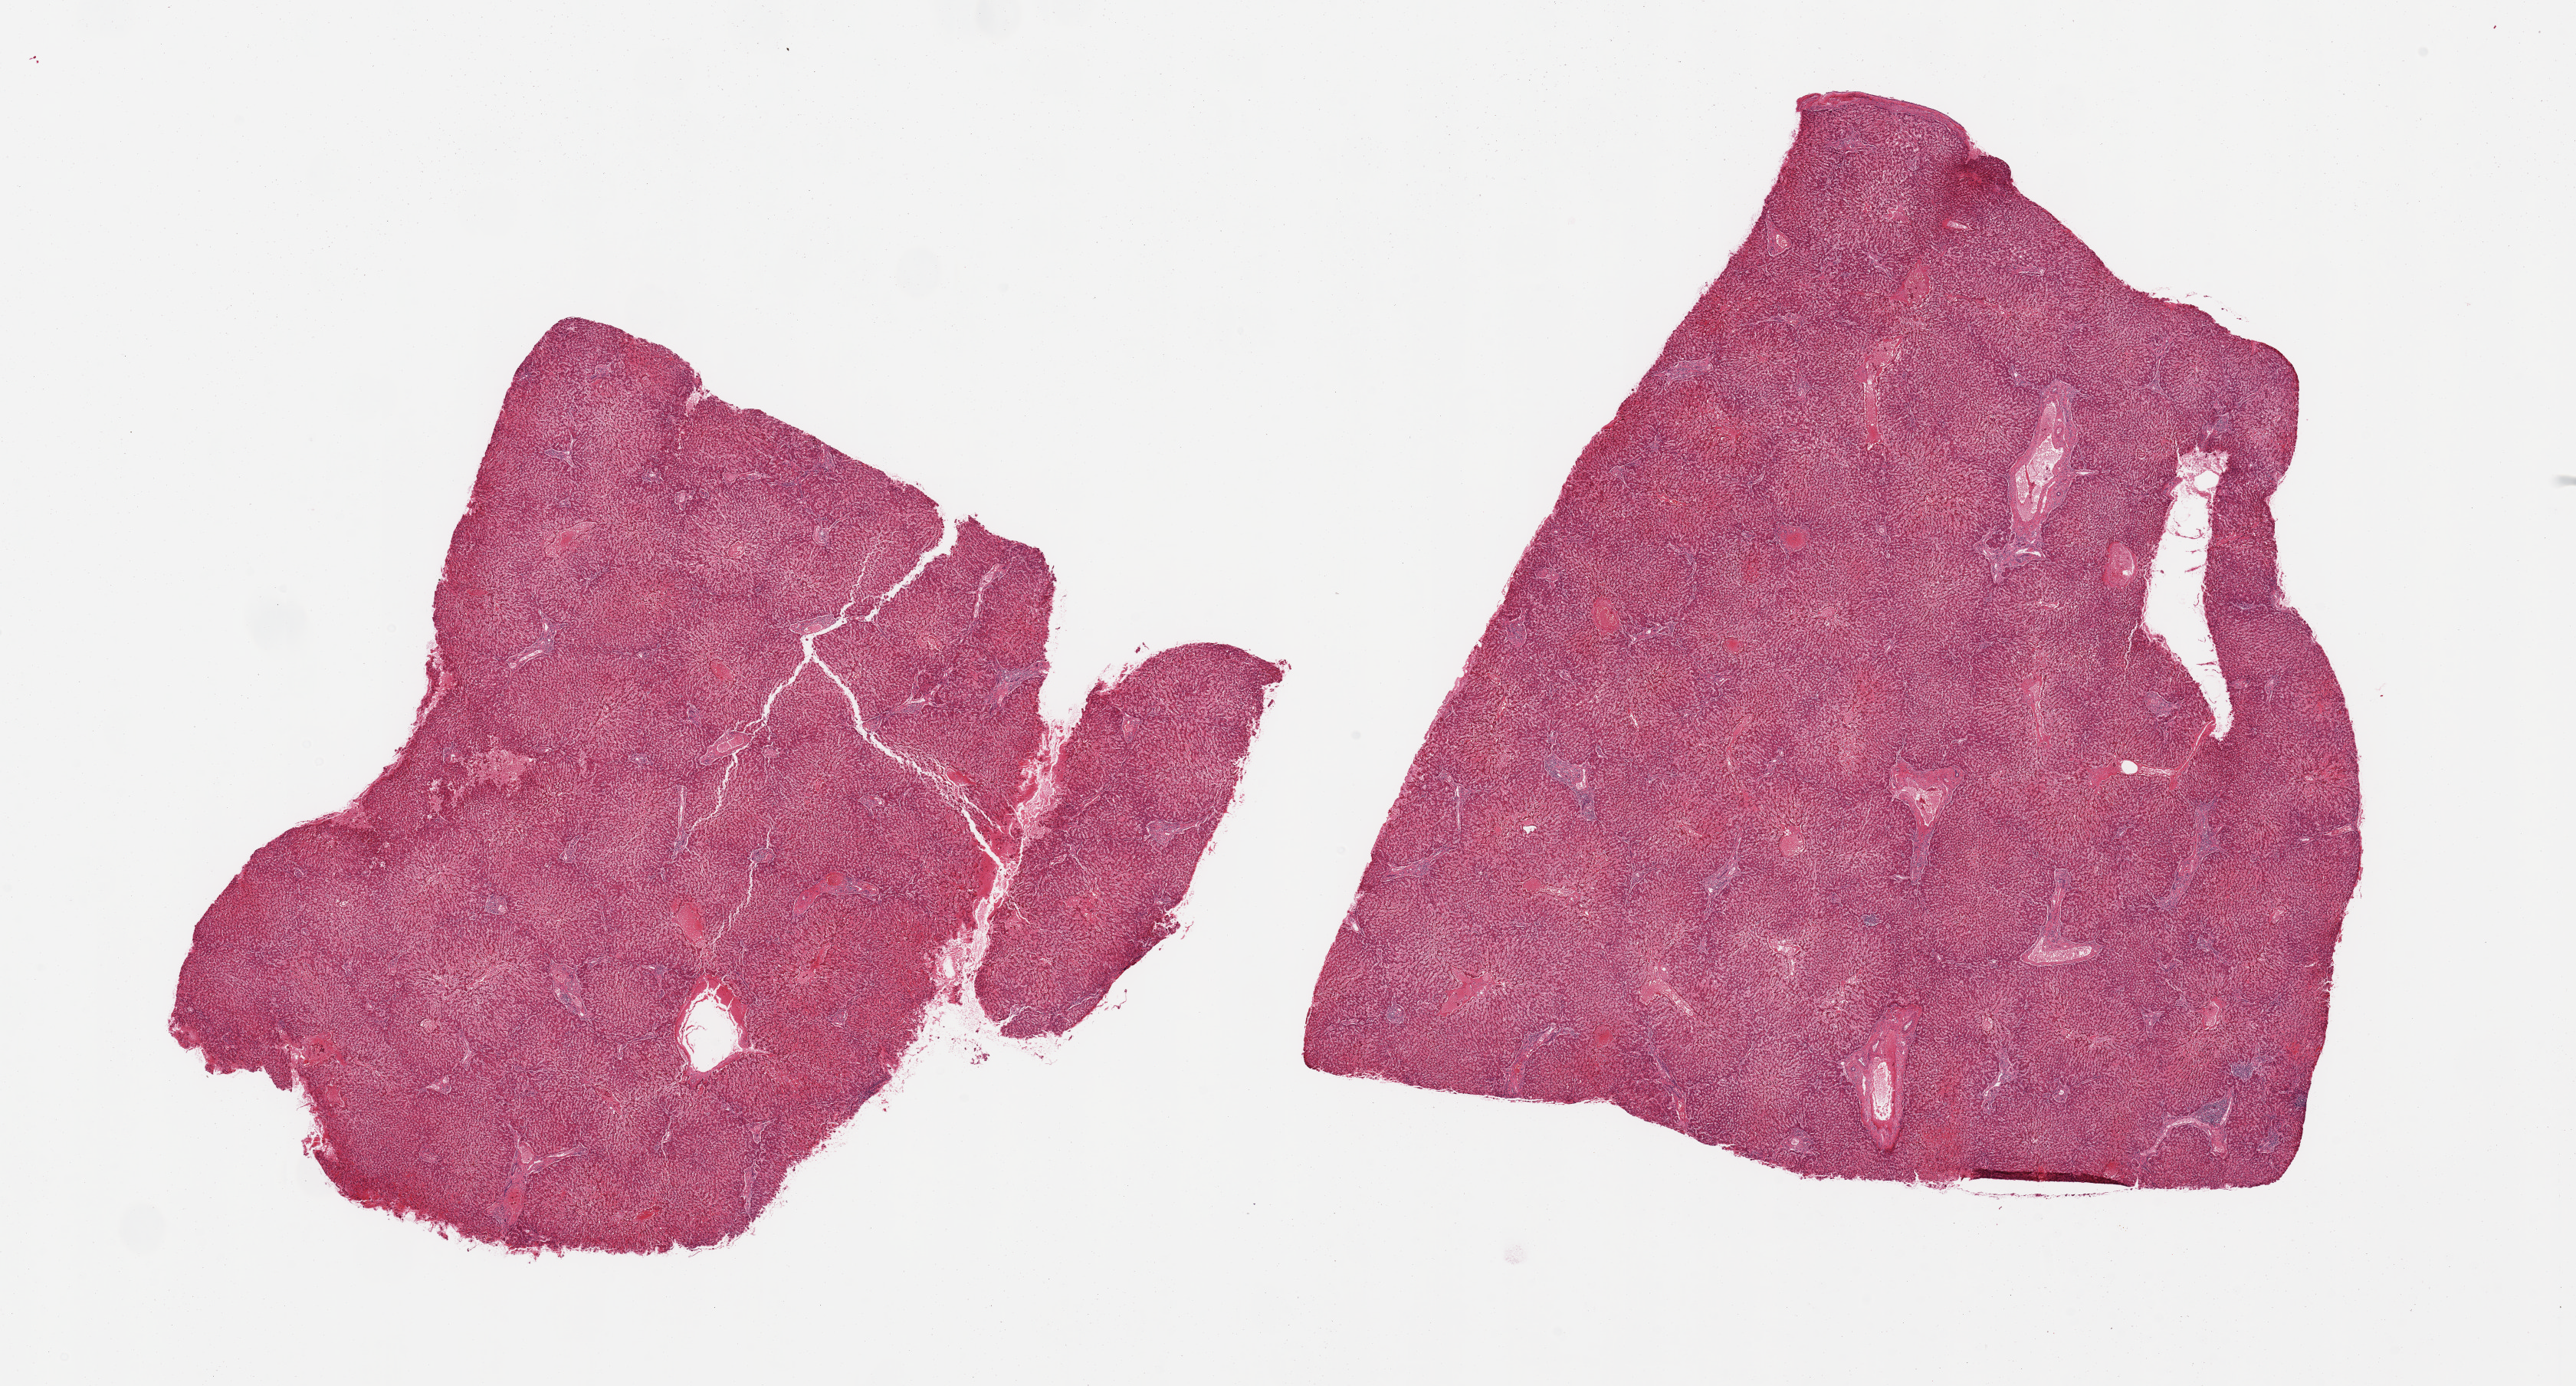
Digitized haematoxylin and eosin-stained section — low-resolution overview of the scanned area, about 26.6 x 14.3 mm (acquisition: 20x scan); PAXgene-fixed, paraffin-embedded tissue; sampled site (target tissue): liver; tissue donor sample. Donor sex: male.
• review note (as recorded): 2 pieces; slight to moderate increase of portal lymphocytes, but no necrosis